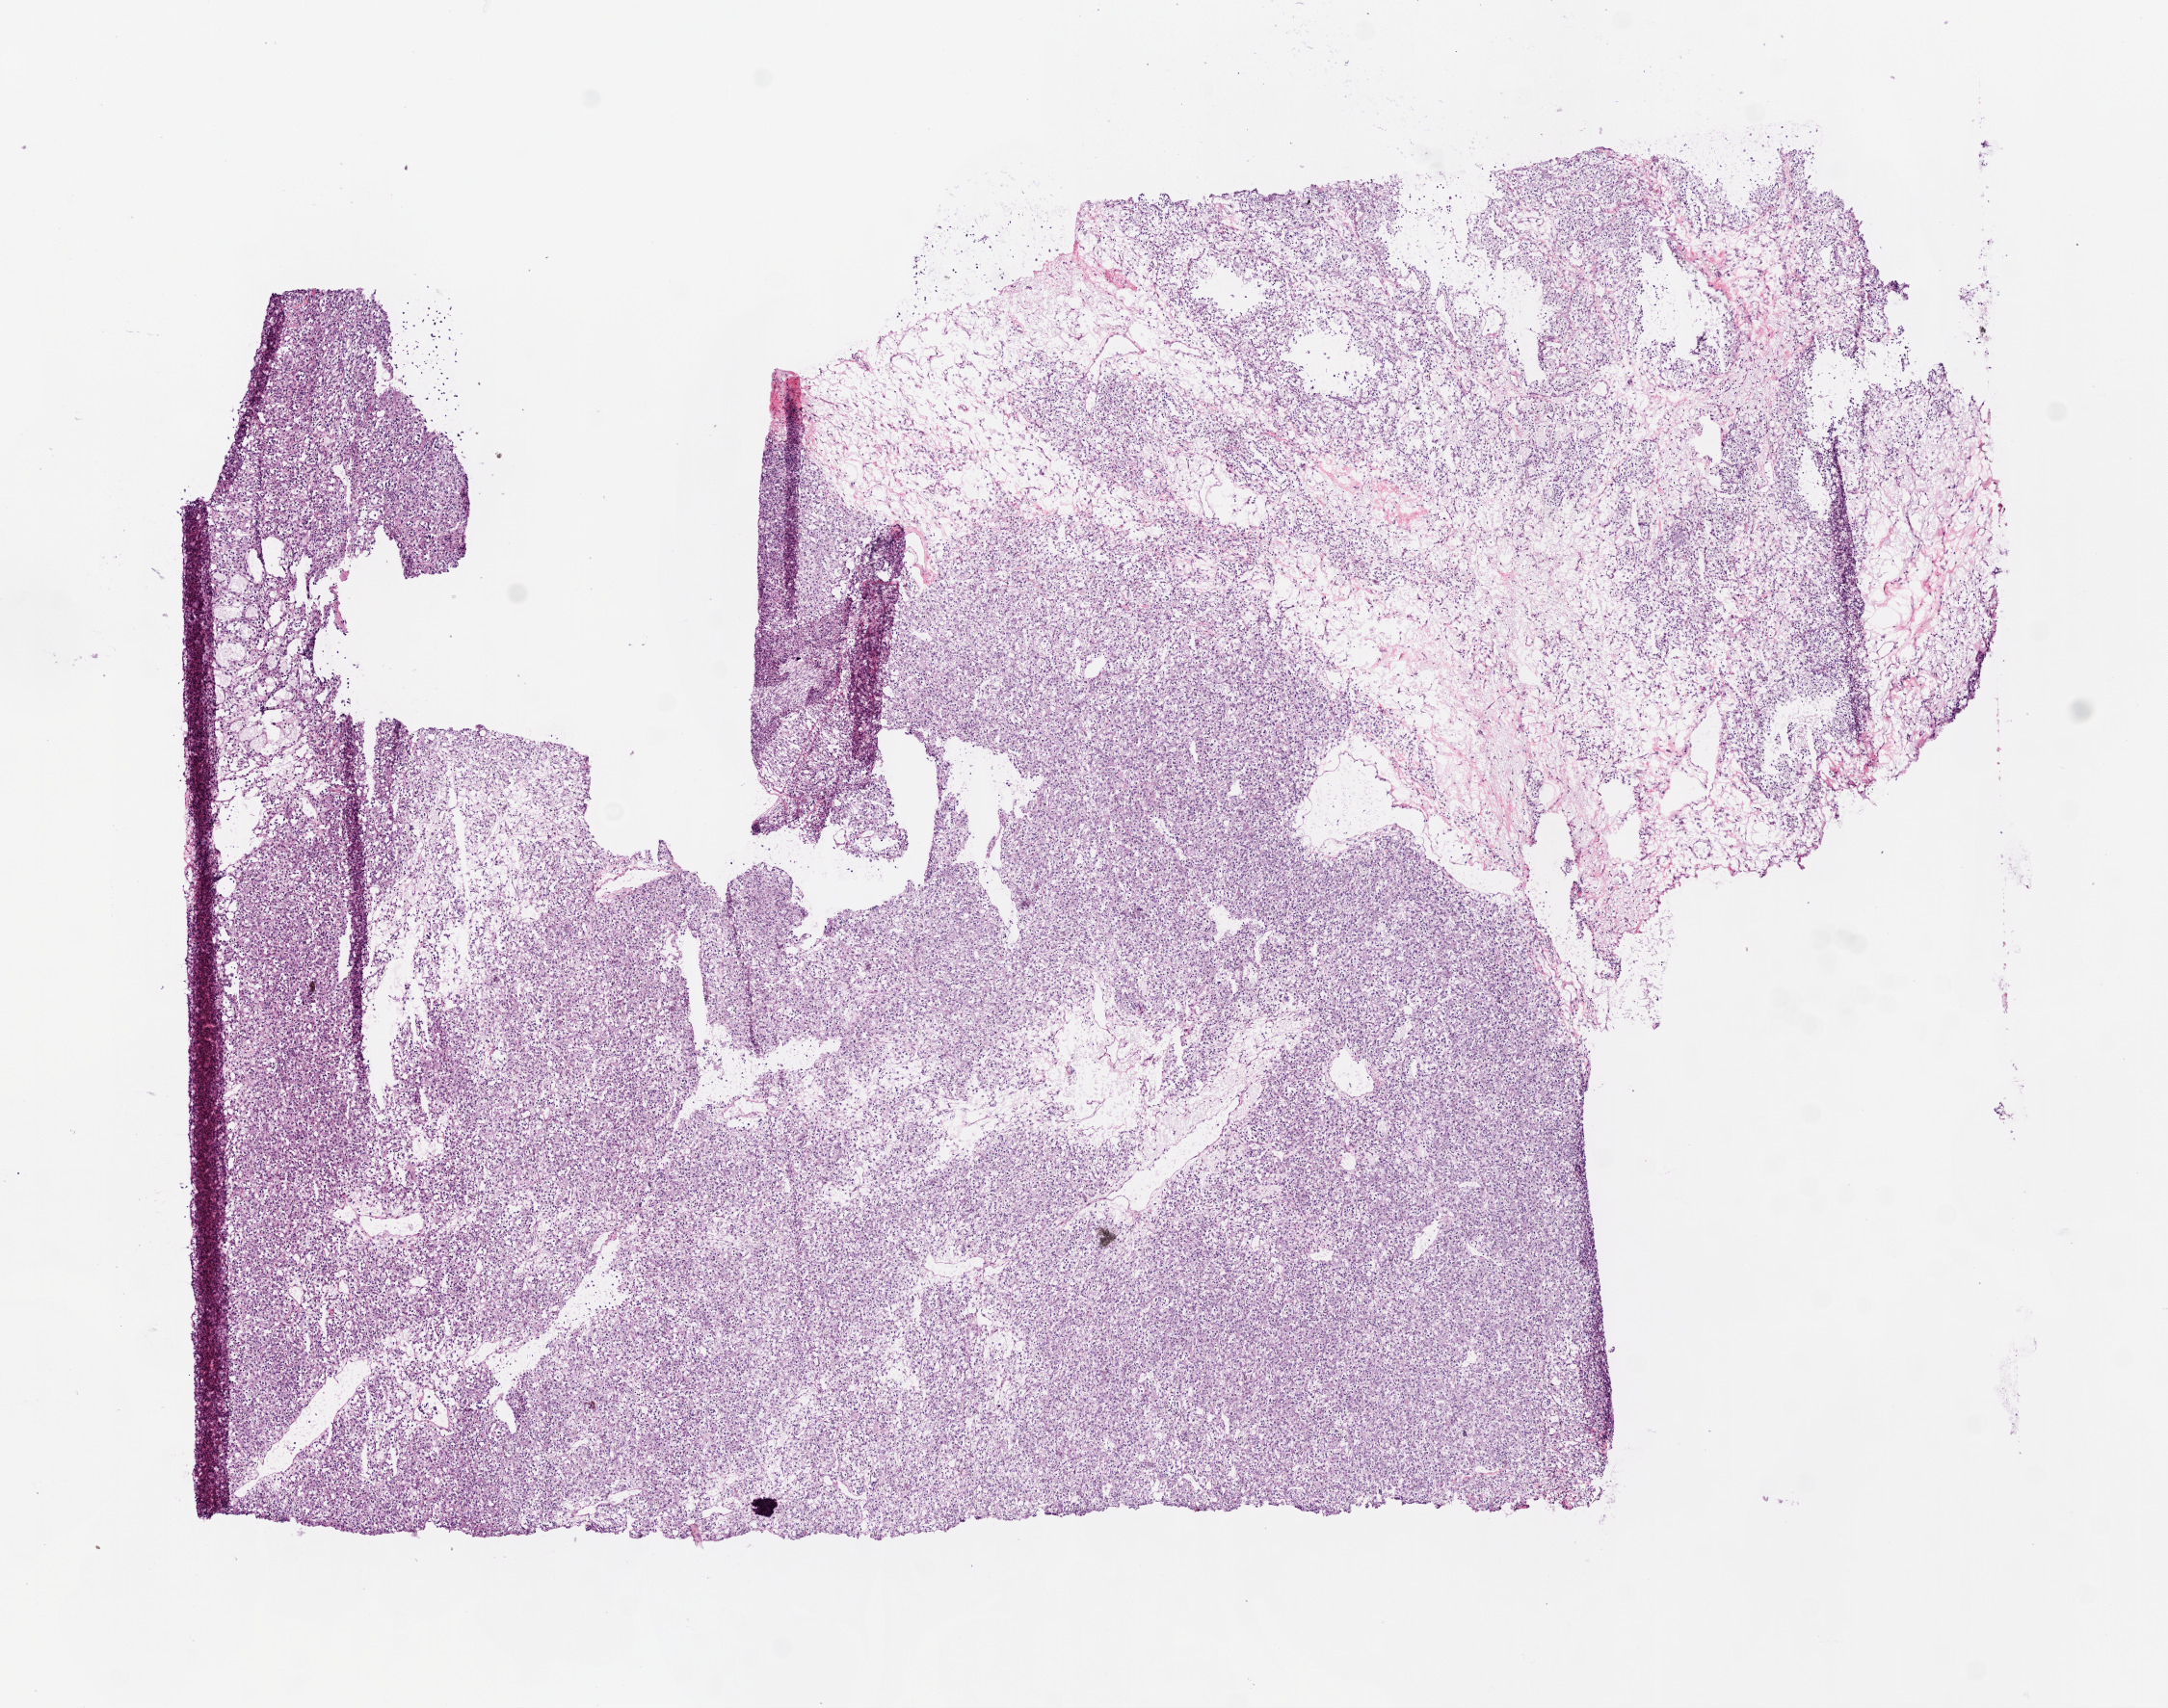
Digitized H&E tissue section (whole slide), shown as a low-resolution overview of the whole scanned area (about 9.0 x 7.1 mm, acquisition: 20x scan), frozen section, kidney, primary tumour sample. Male patient; age at initial diagnosis 83 years. Pathologist review of this section (percent, as recorded): tumour cells 100%, tumour nuclei 99%.
Diagnosis: Clear cell adenocarcinoma, NOS.